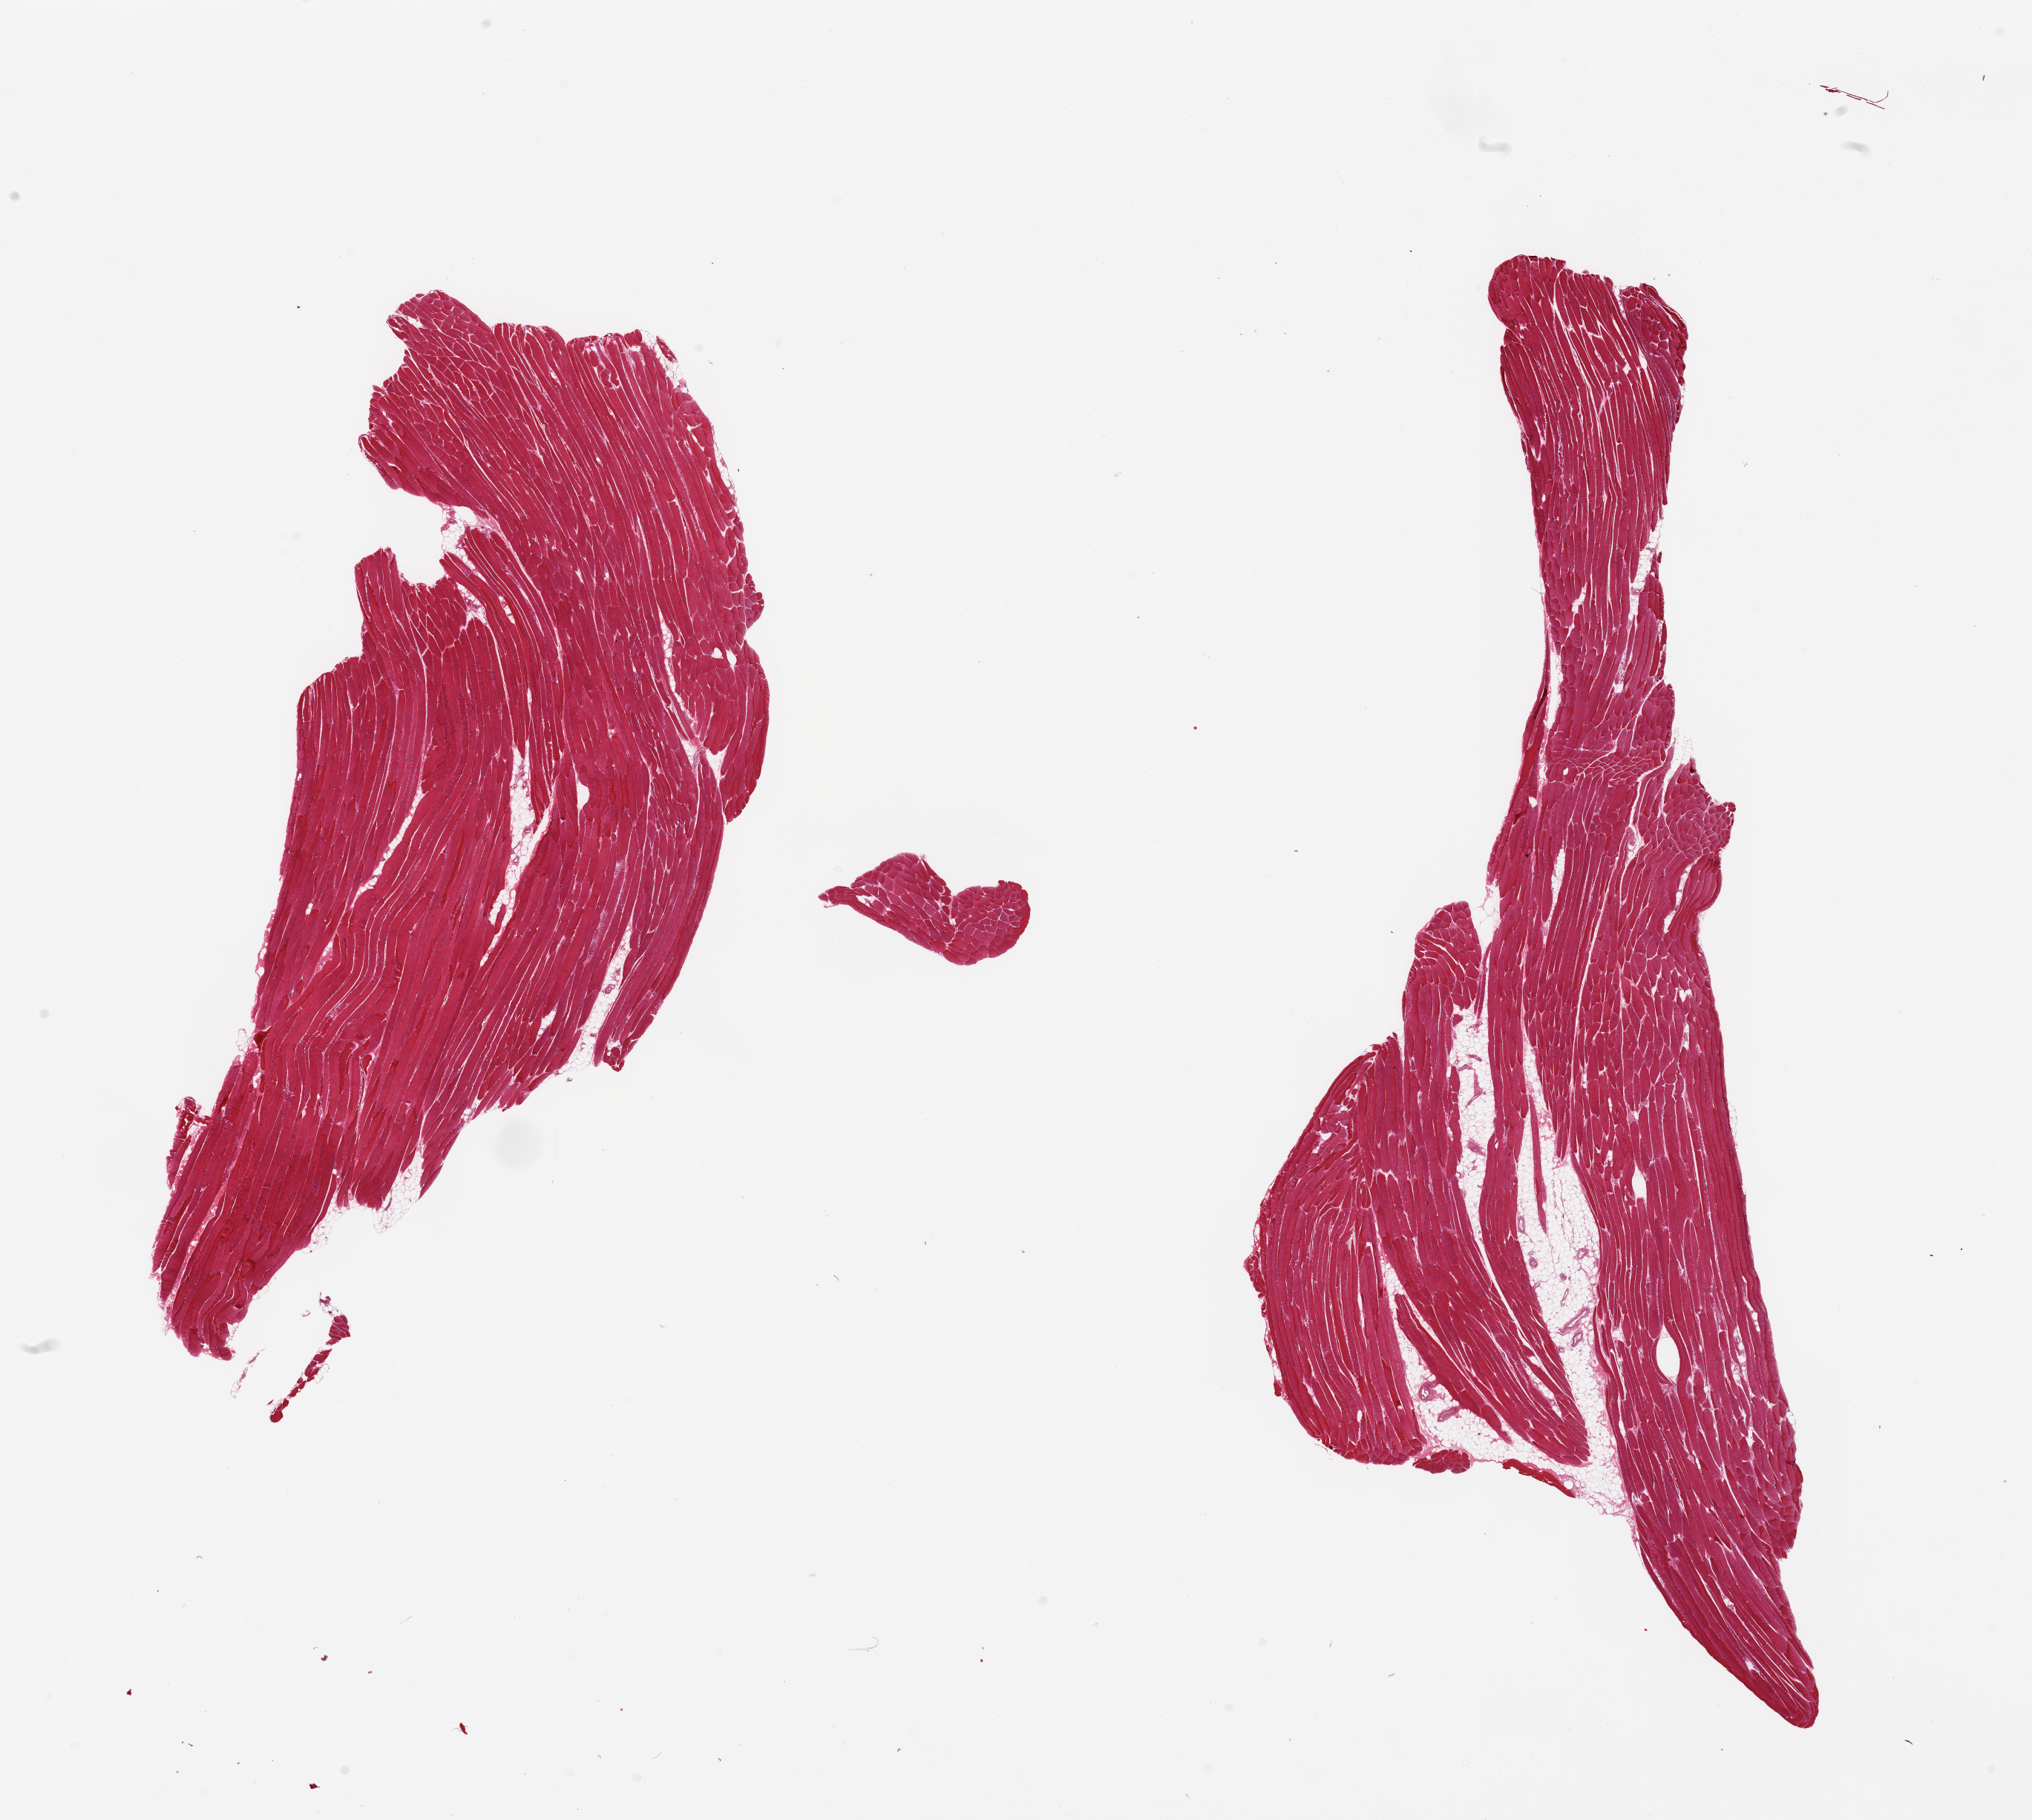
Whole-slide image, haematoxylin and eosin stain, shown as a low-resolution overview of the whole scanned area (about 21.7 x 19.4 mm); PAXgene-fixed paraffin-embedded (PFPE) section; section of skeletal muscle (target tissue); tissue donor sample. Donor: male.
• reviewer comment on this tissue sample: 2 pieces; 10 & 5% internal fat